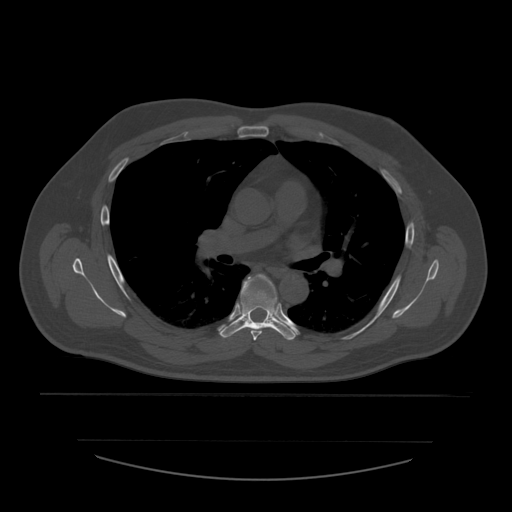
CT including the spine, one axial slice; position 385 of 532 along the scan axis; reconstruction kernel STANDARD; 120 kVp; bone window (W 1800 / L 400 HU); 1.25 mm slice thickness; 512 × 512 image matrix, field of view 441 × 441 mm. Patient age 44 years. Case-level facts recorded for this patient, not image findings: primary cancer: soft tissue sarcoma.
Outlined on this slice (semi-automatically segmented with operator editing):
- T5 vertebra: box from (x=249, y=275) to (x=277, y=341) px
- T6 vertebra: (x=220, y=275)–(x=298, y=341)